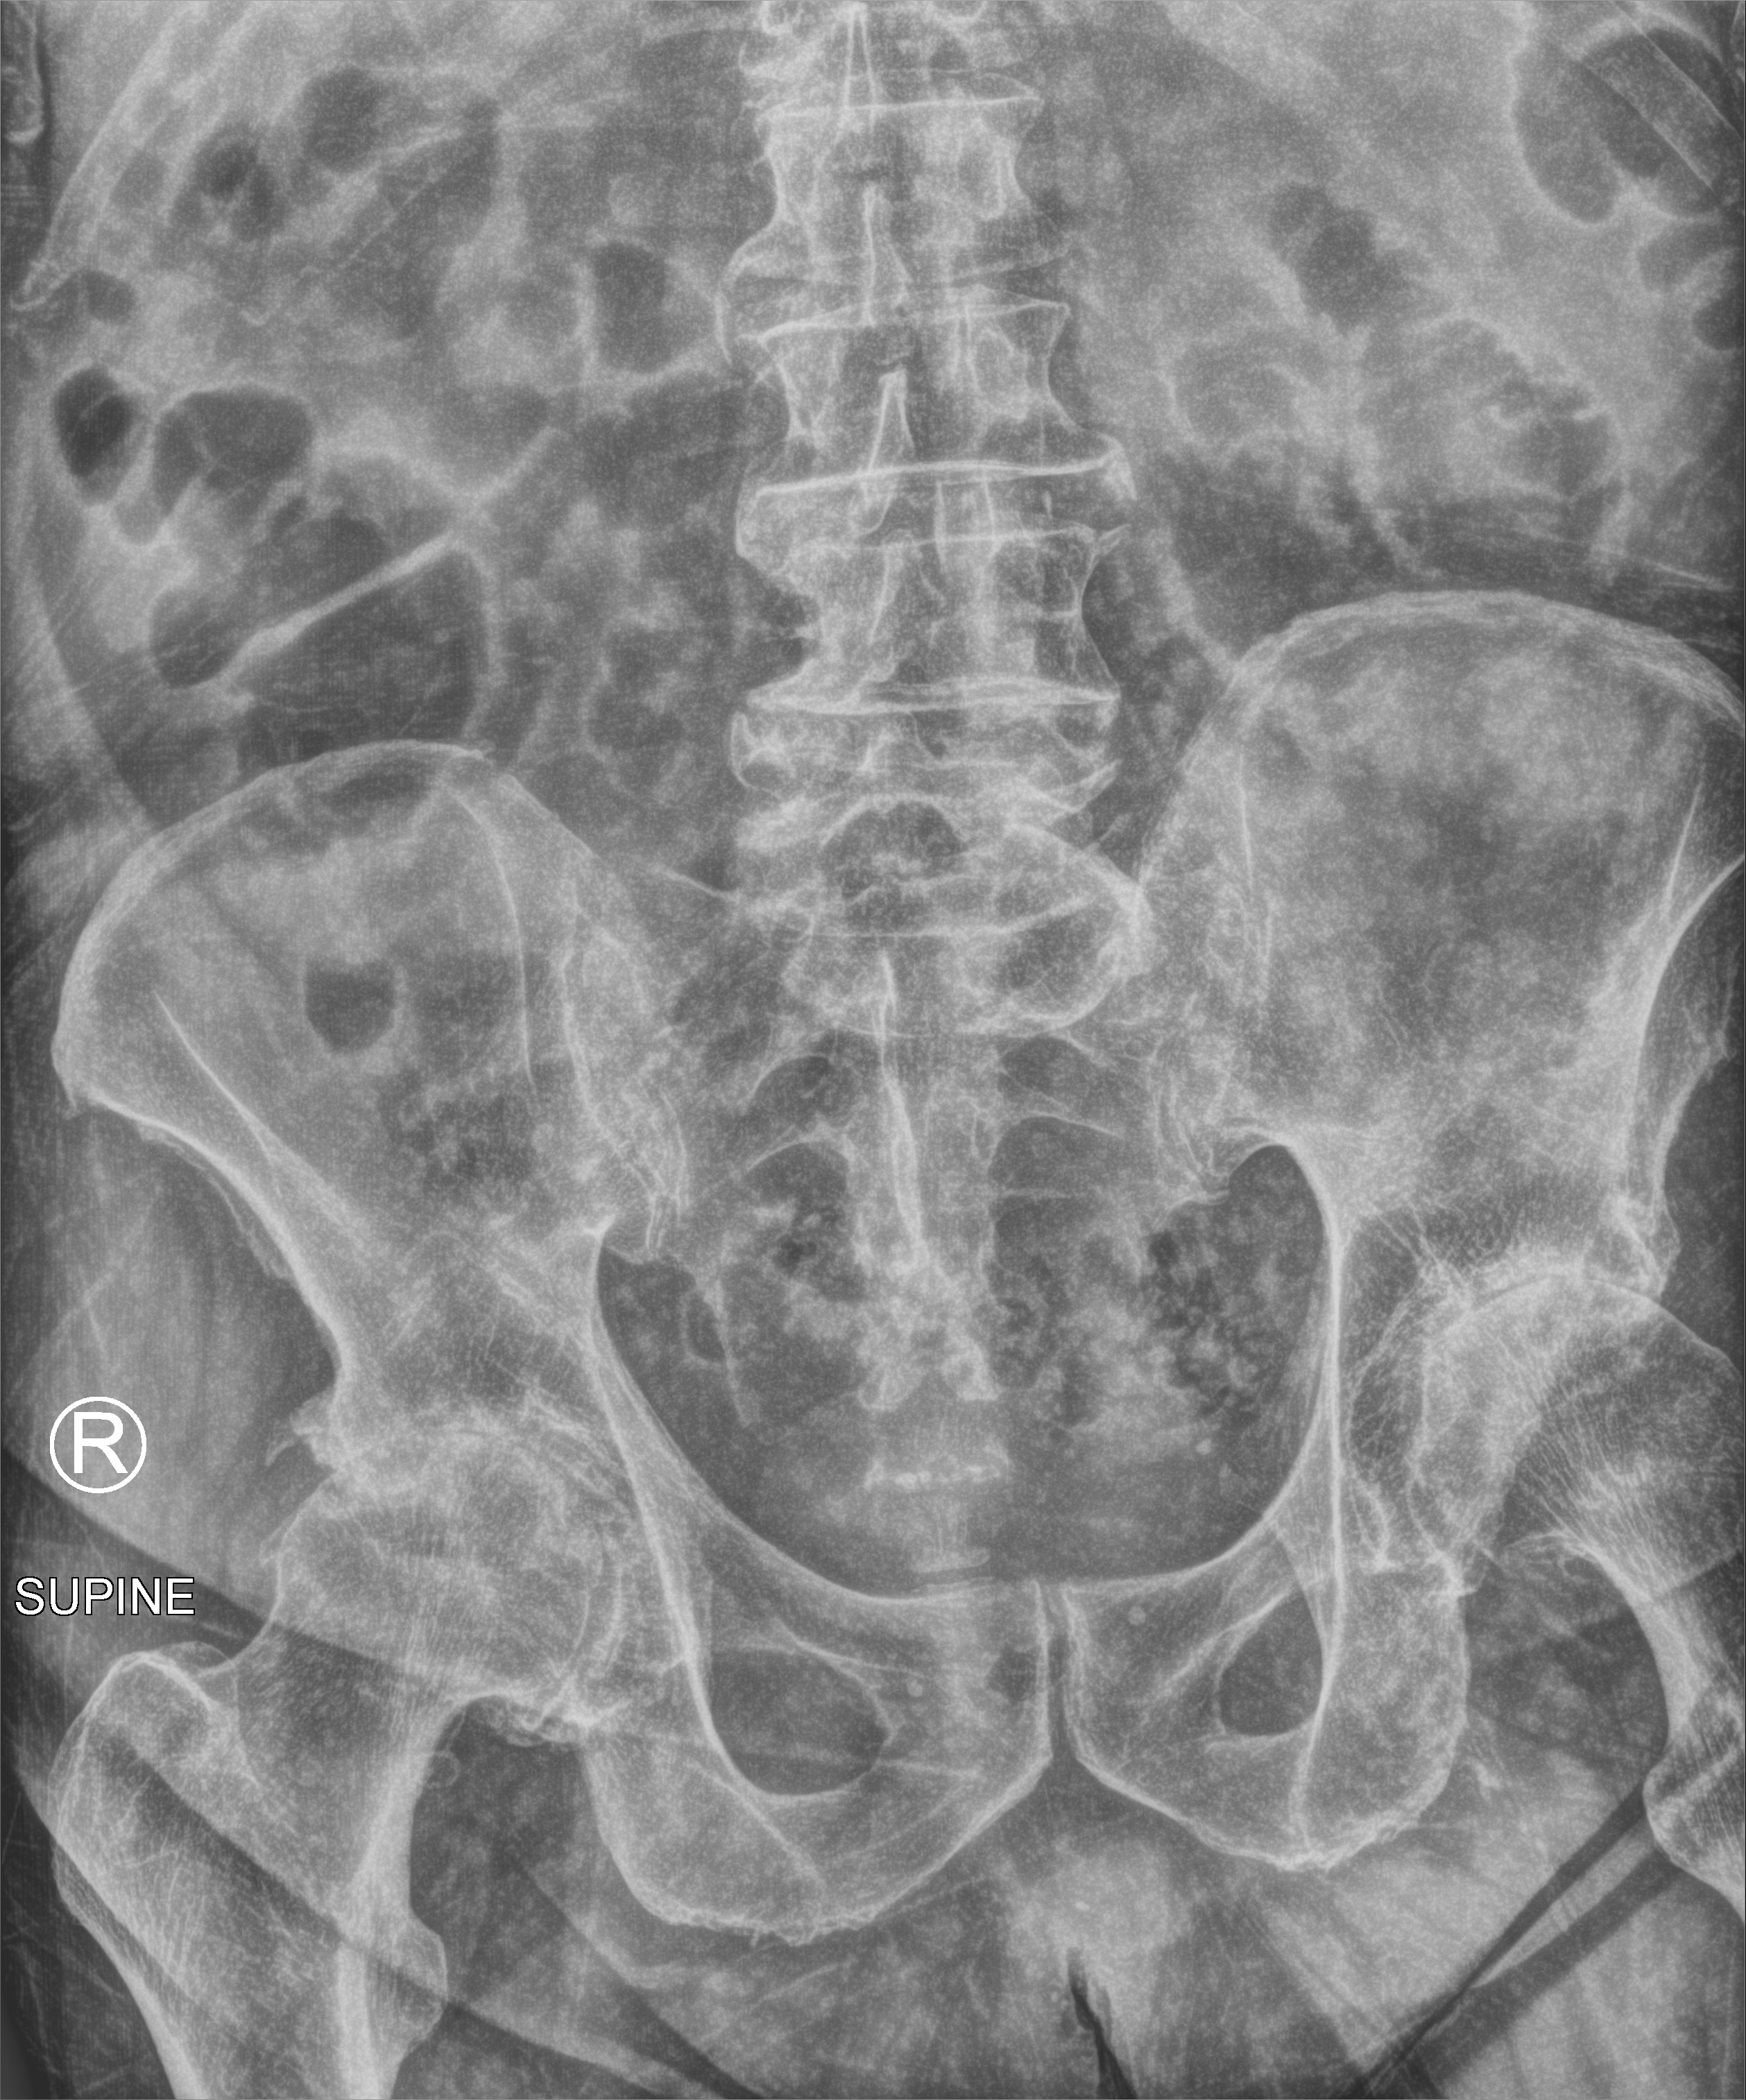
Bedside abdomen radiograph (computed radiography); anteroposterior (AP) projection. Patient hospitalised with COVID-19; male, aged 75–90 years.
From the hospital-stay record, not from the radiograph (when in the stay this image was taken is not recorded): length of hospital stay: 5 days; other chronic lung disease (admission record): no.